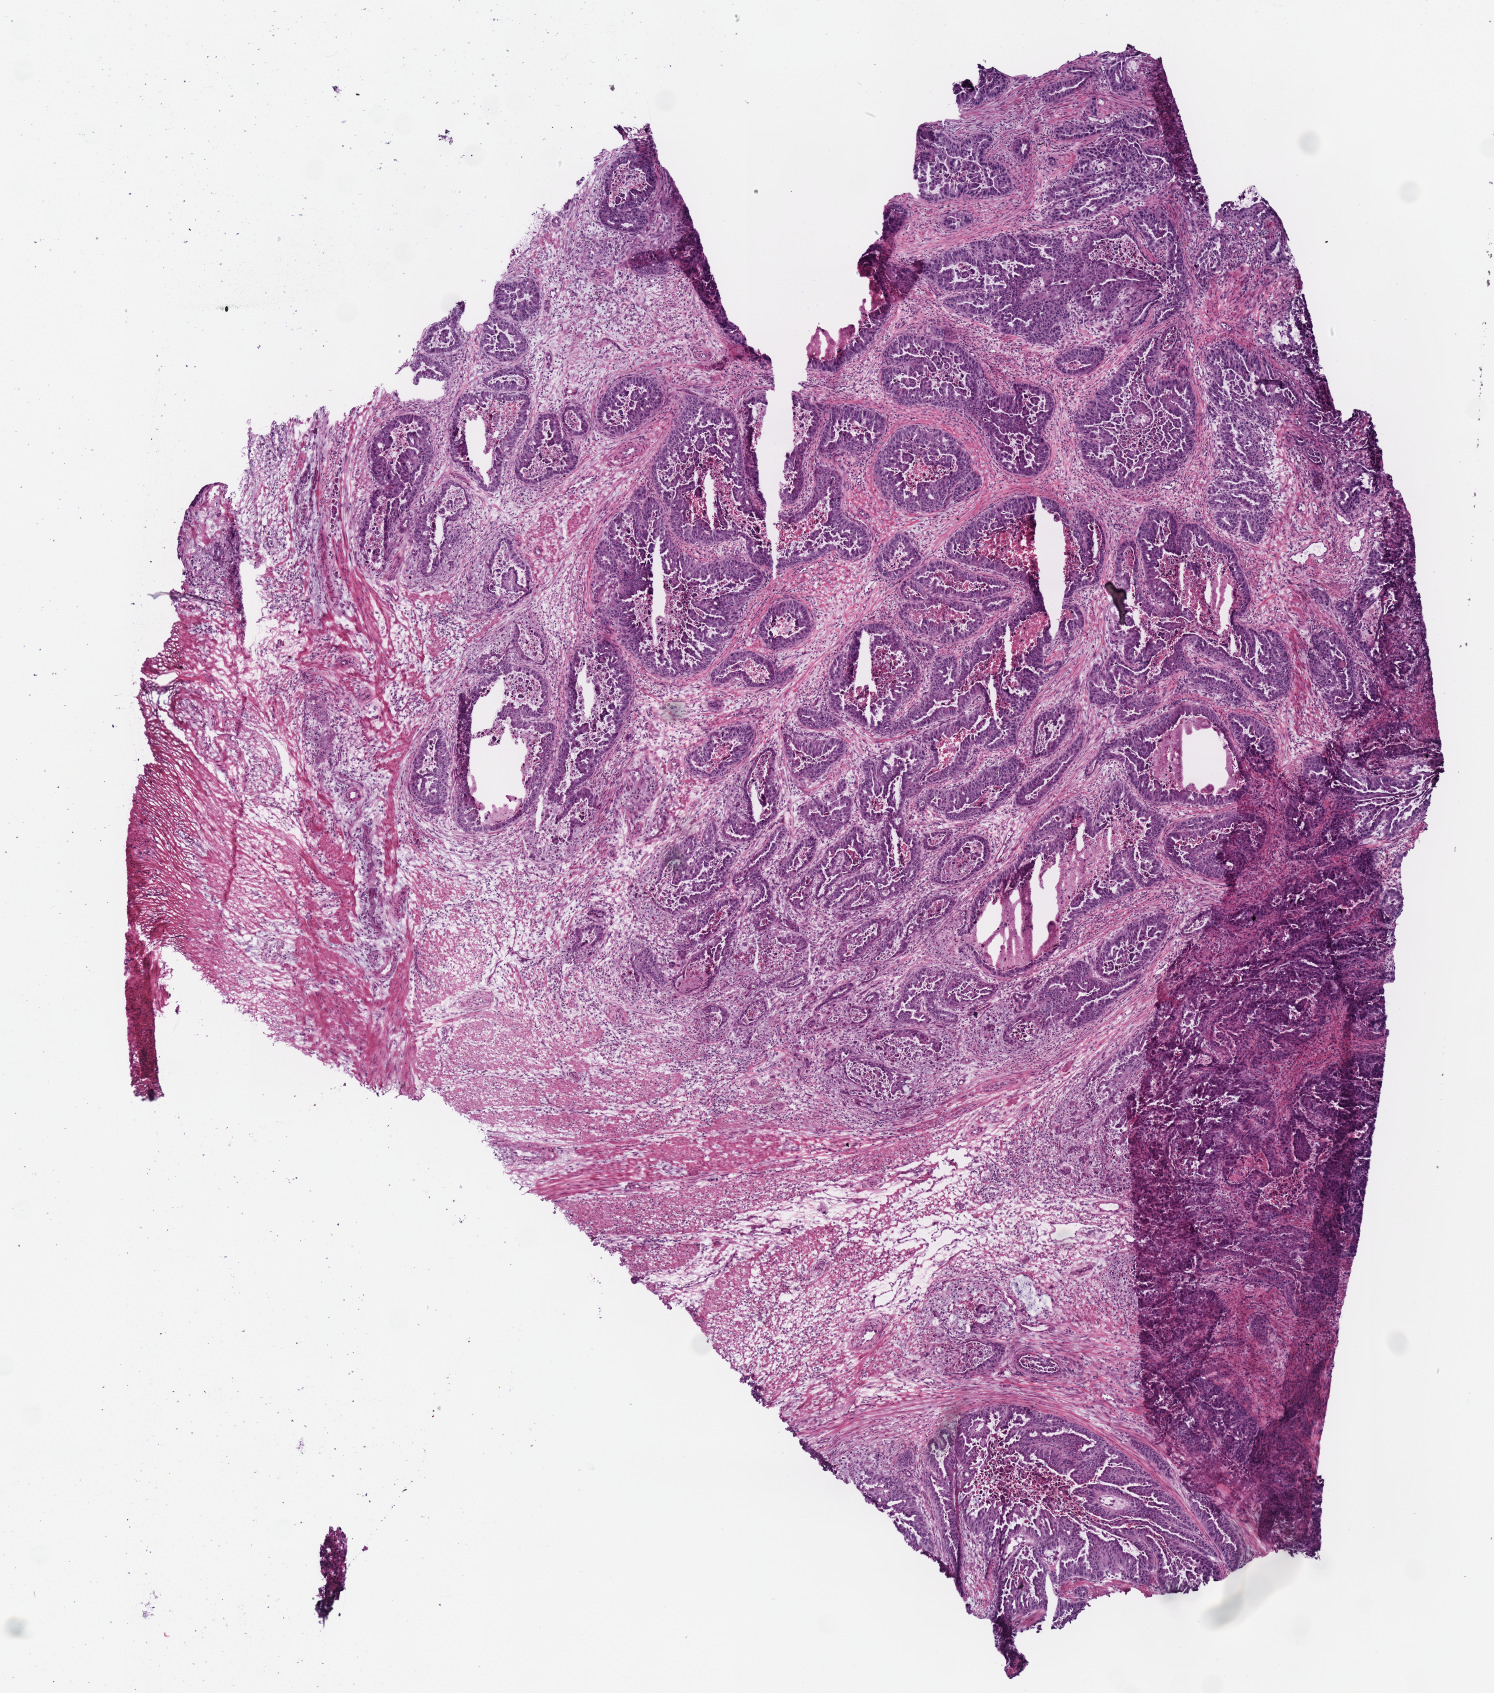
Whole-slide histology image, H&E — low-resolution overview of the scanned area, about 5.9 x 6.7 mm (acquisition: 40x scan), frozen section from the bottom of the tissue portion, primary tumour sample from the stomach. Female, age 71 years at initial diagnosis. Histologic grade: G3 (poorly differentiated). Slide review estimates, as recorded: tumour cells 85%, tumour nuclei 80%, normal cells 10%, stromal cells 0%, necrosis 5%. Inflammatory infiltration, as recorded: lymphocyte infiltration 2%, monocyte infiltration 0%, neutrophil infiltration 15%.
Lymph nodes positive (case pathology): 2 of 19 examined. Histologic diagnosis: Adenocarcinoma, intestinal type (gastric antrum). AJCC pathologic stage: IIB.